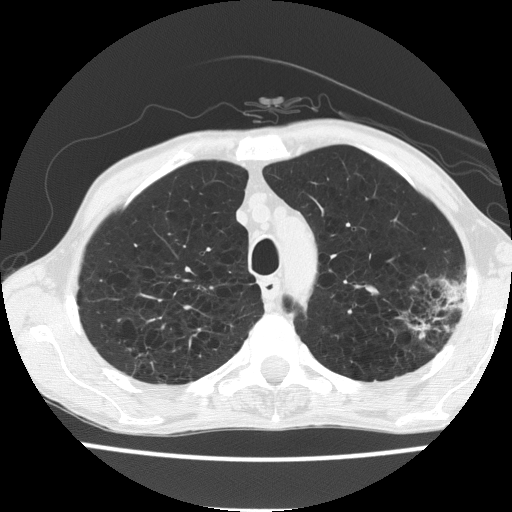
Chest CT (low-dose screening protocol), one axial image. First (baseline) screen. Lung window (W 1500 / L -600 HU). 120 kVp. Slice 42 of 187 in the series. Male participant, aged 60 years at enrolment.
Expert-annotated lung lesion, bounding box <393,266,469,344> (left, top, right, bottom; pixels). Screening reader's record for this exam: no non-calcified nodule ≥4 mm recorded. Lung cancer was diagnosed 490 days after this screen: bronchiolo-alveolar carcinoma, mucinous, left upper lobe, stage IV (AJCC 6th edition).